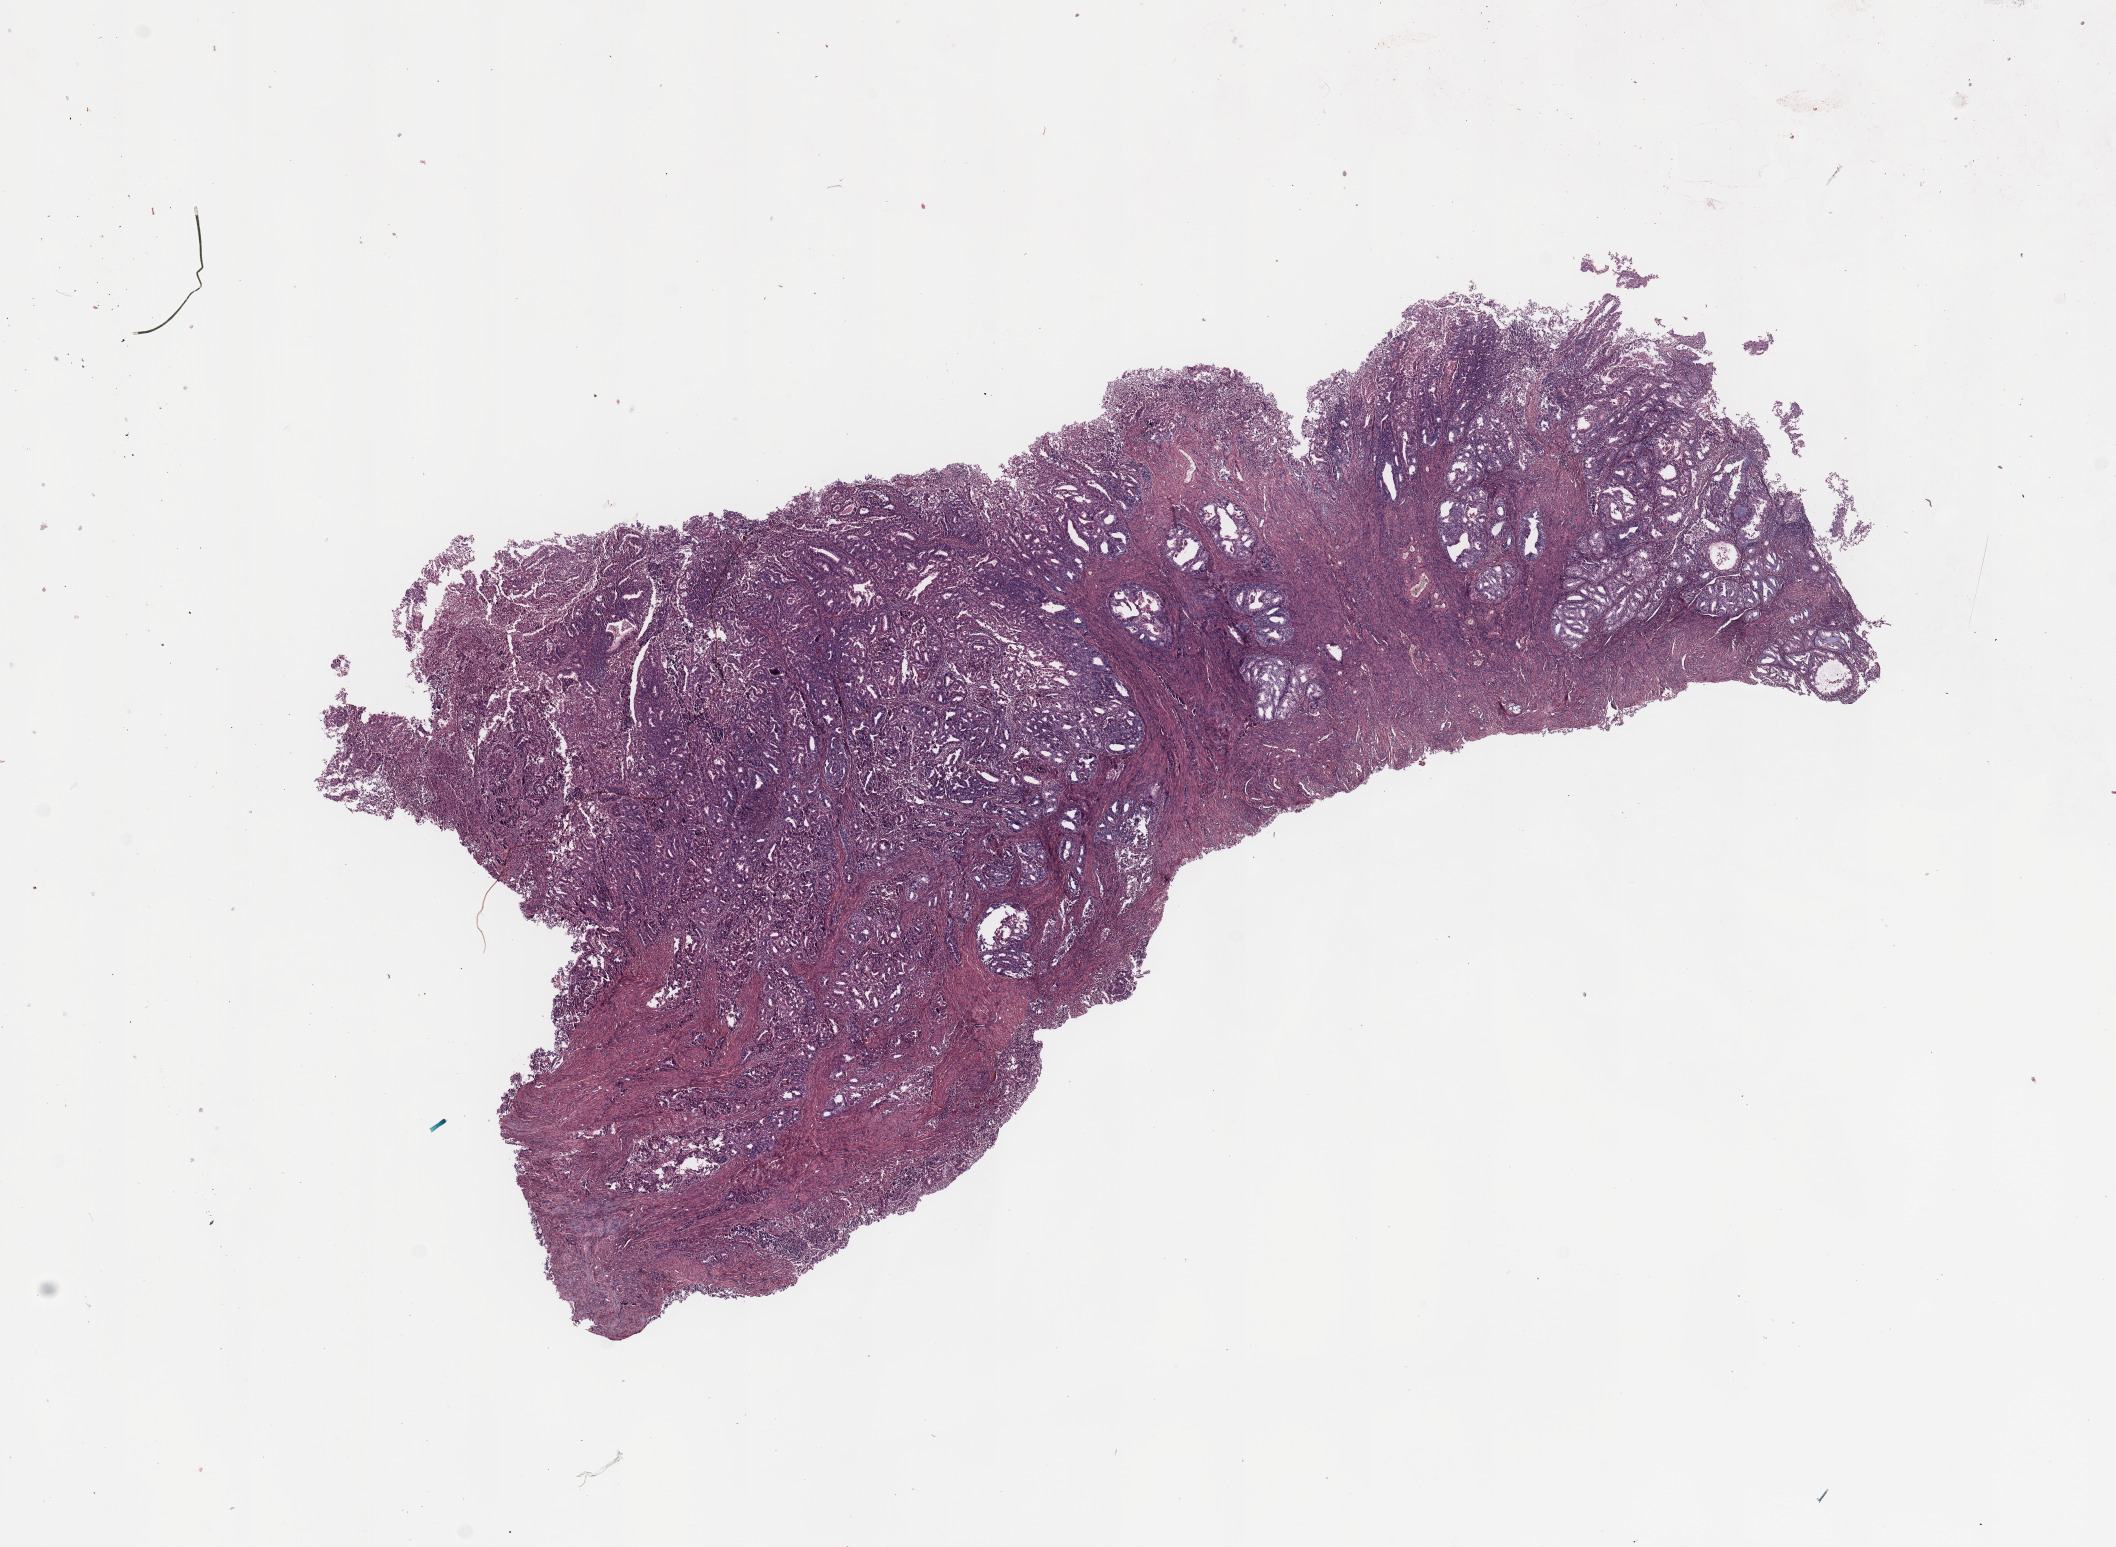
Whole-slide histology image, H&E-stained, shown as a low-resolution overview of the whole scanned area (about 16.7 x 12.2 mm); tumour tissue sample, sampled site: uterus. Patient: female, age 70 years. Histologic grade: G2 (moderately differentiated). Pathologist review of this section (percent, as recorded): tumour nuclei 90%, necrosis 0%.
* AJCC pathologic stage: I
* diagnosis: Endometrioid adenocarcinoma, NOS